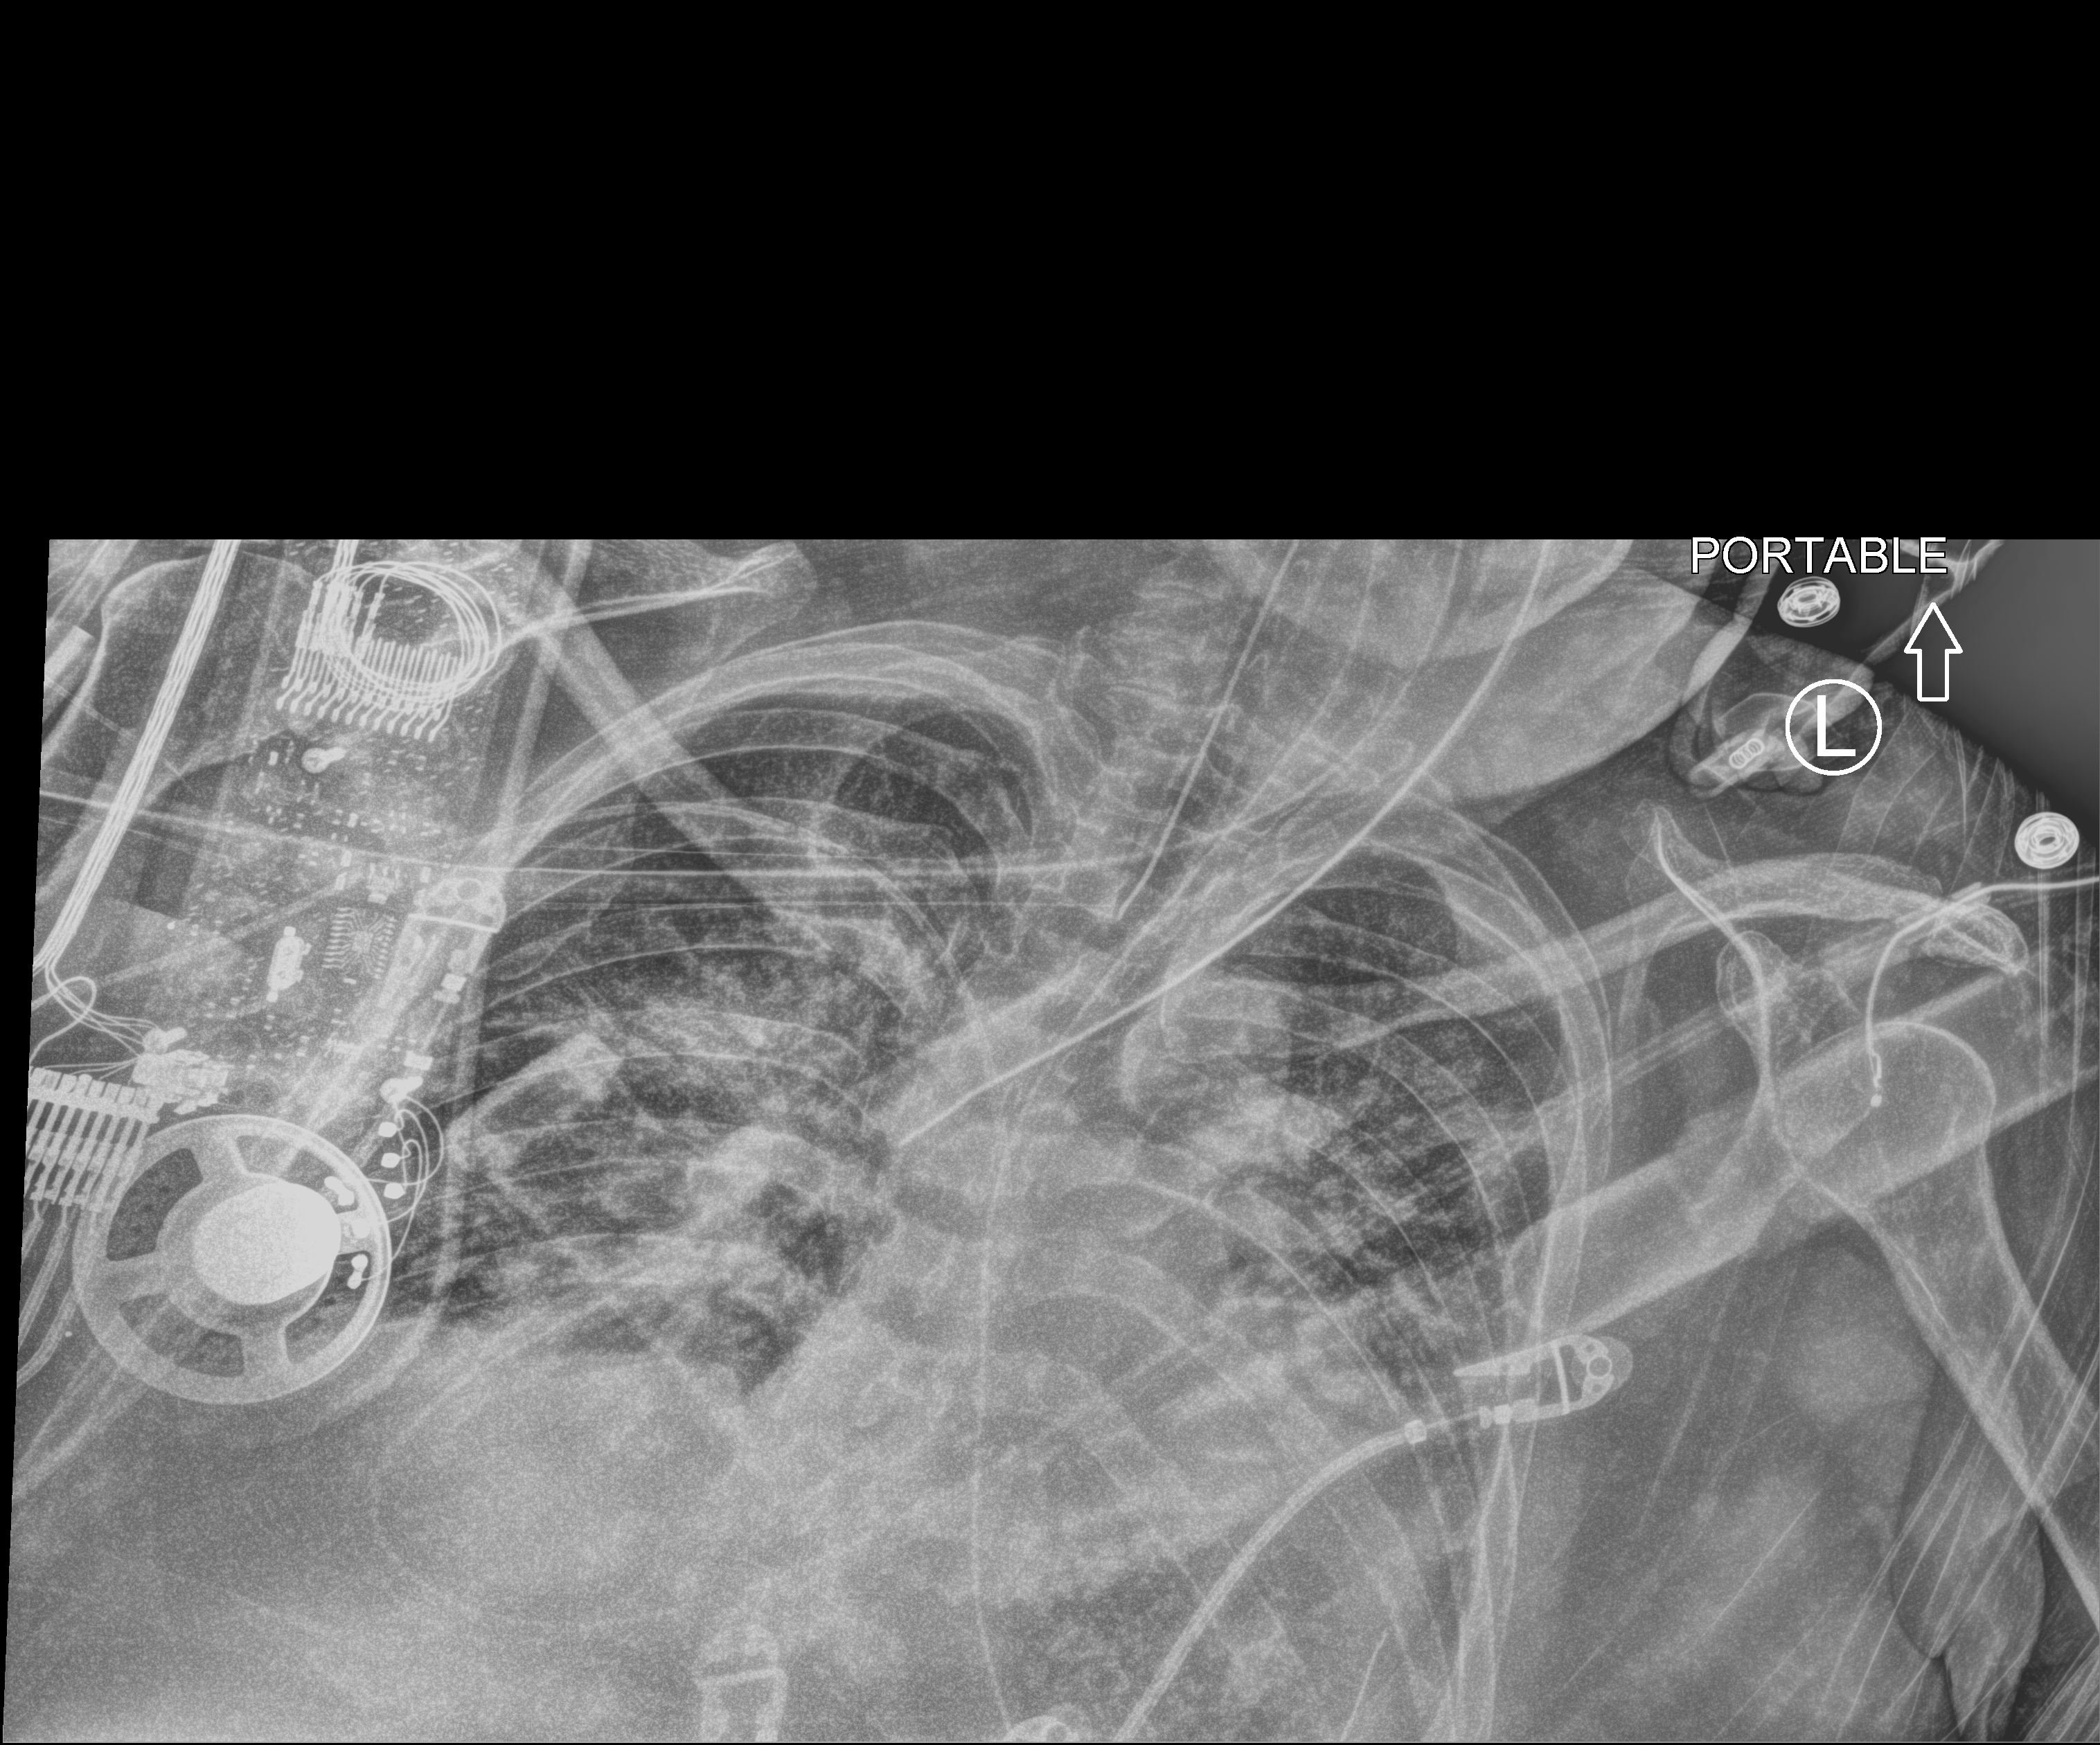
Bedside chest radiograph (computed radiography), anteroposterior (AP) projection. Patient hospitalised with COVID-19, aged 18–59 years.
From the hospital-stay record, not from the radiograph (when in the stay this image was taken is not recorded): admitted to intensive care during this hospital stay: yes; mechanically ventilated during this hospital stay: yes; length of hospital stay: 15 days.